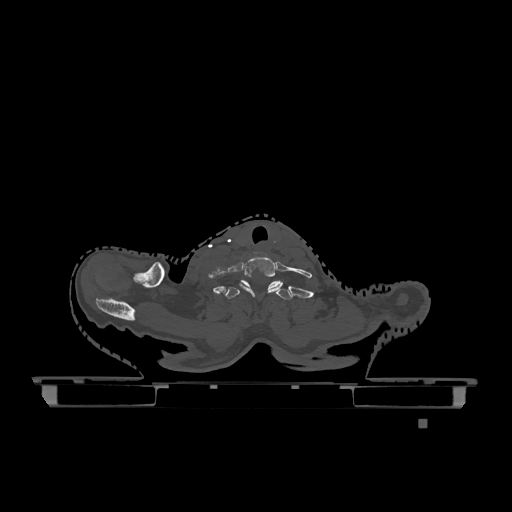
CT including the spine, one axial slice. Position 1016 of 1317 along the scan axis. Bone window (W 1800 / L 400 HU). 512 × 512 image matrix. Female patient, age 74 years. Case-level facts recorded for this patient, not image findings: primary cancer: lung.
Structures marked on this image (semi-automatically segmented with operator editing):
- T1 vertebra: bounding box (x1, y1, x2, y2) in pixels: (224, 280, 292, 300)